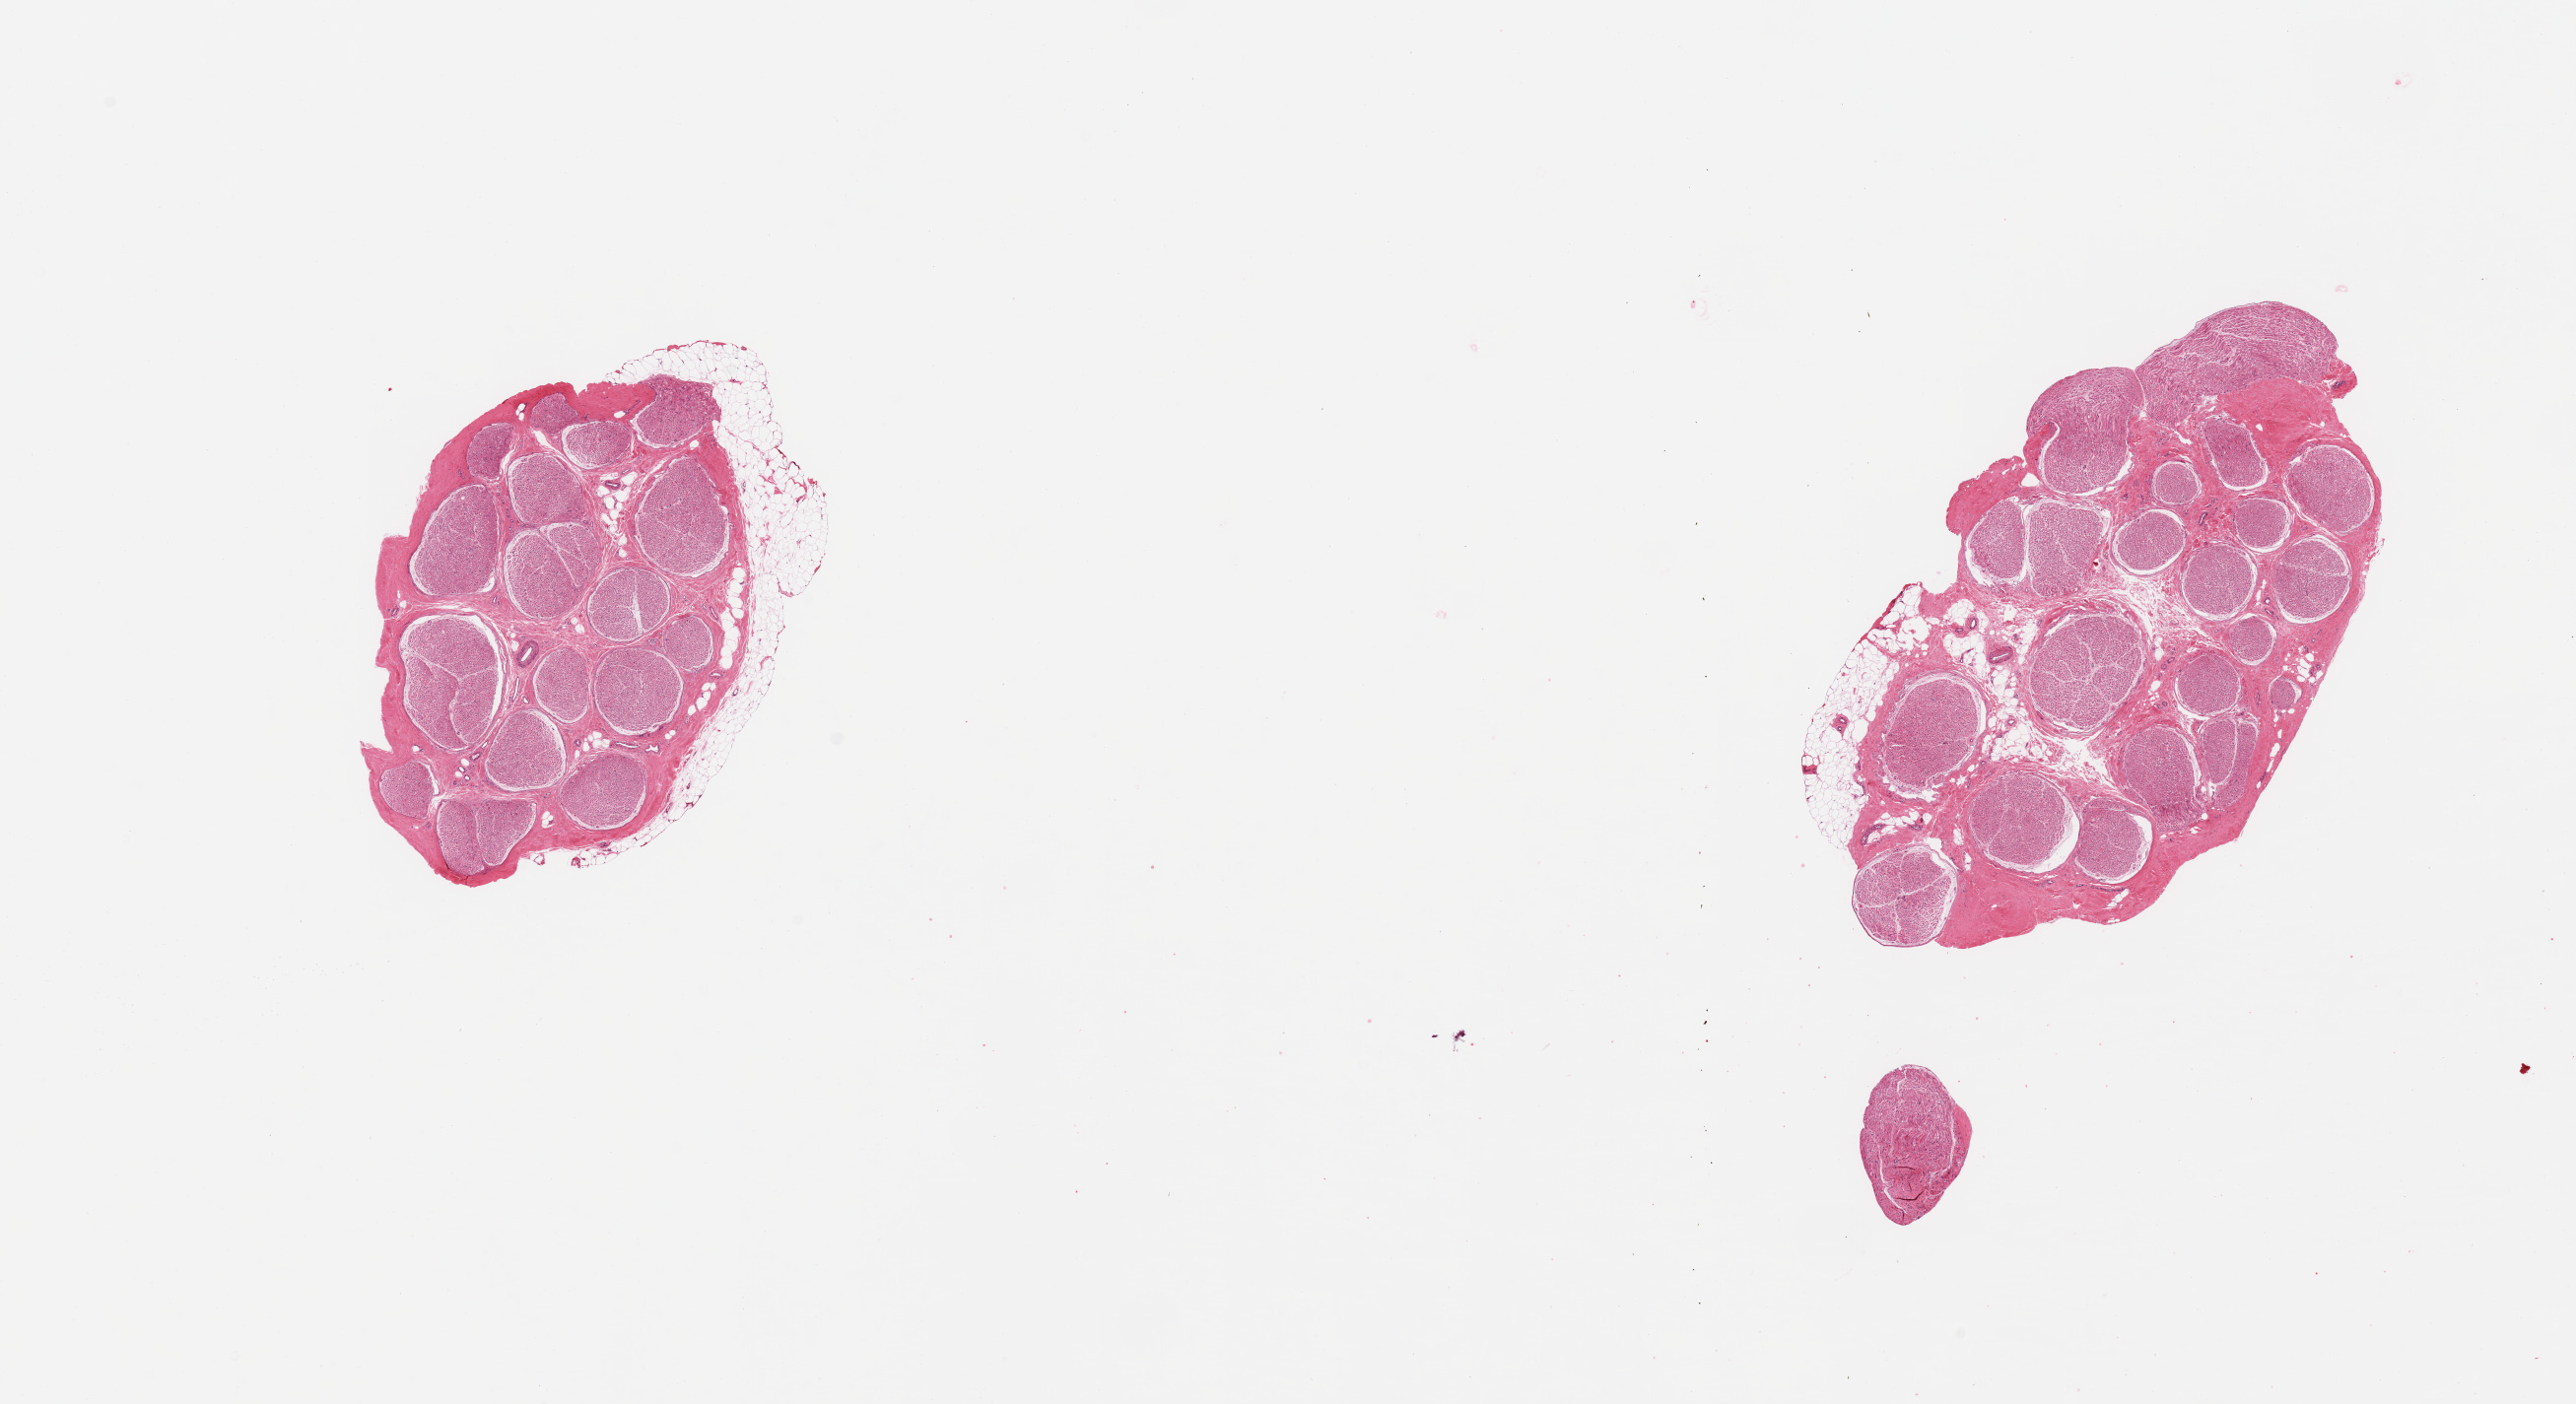
Whole-slide image, haematoxylin and eosin stain, whole scanned area (about 20.7 x 11.3 mm) shown as a low-resolution overview, PAXgene-fixed paraffin-embedded (PFPE) section, section of tibial nerve (target tissue), donor tissue sample. Male donor.
Reviewer comment on this tissue sample: 2 pieces; small attachment of fat on both pieces (up to ~10%).